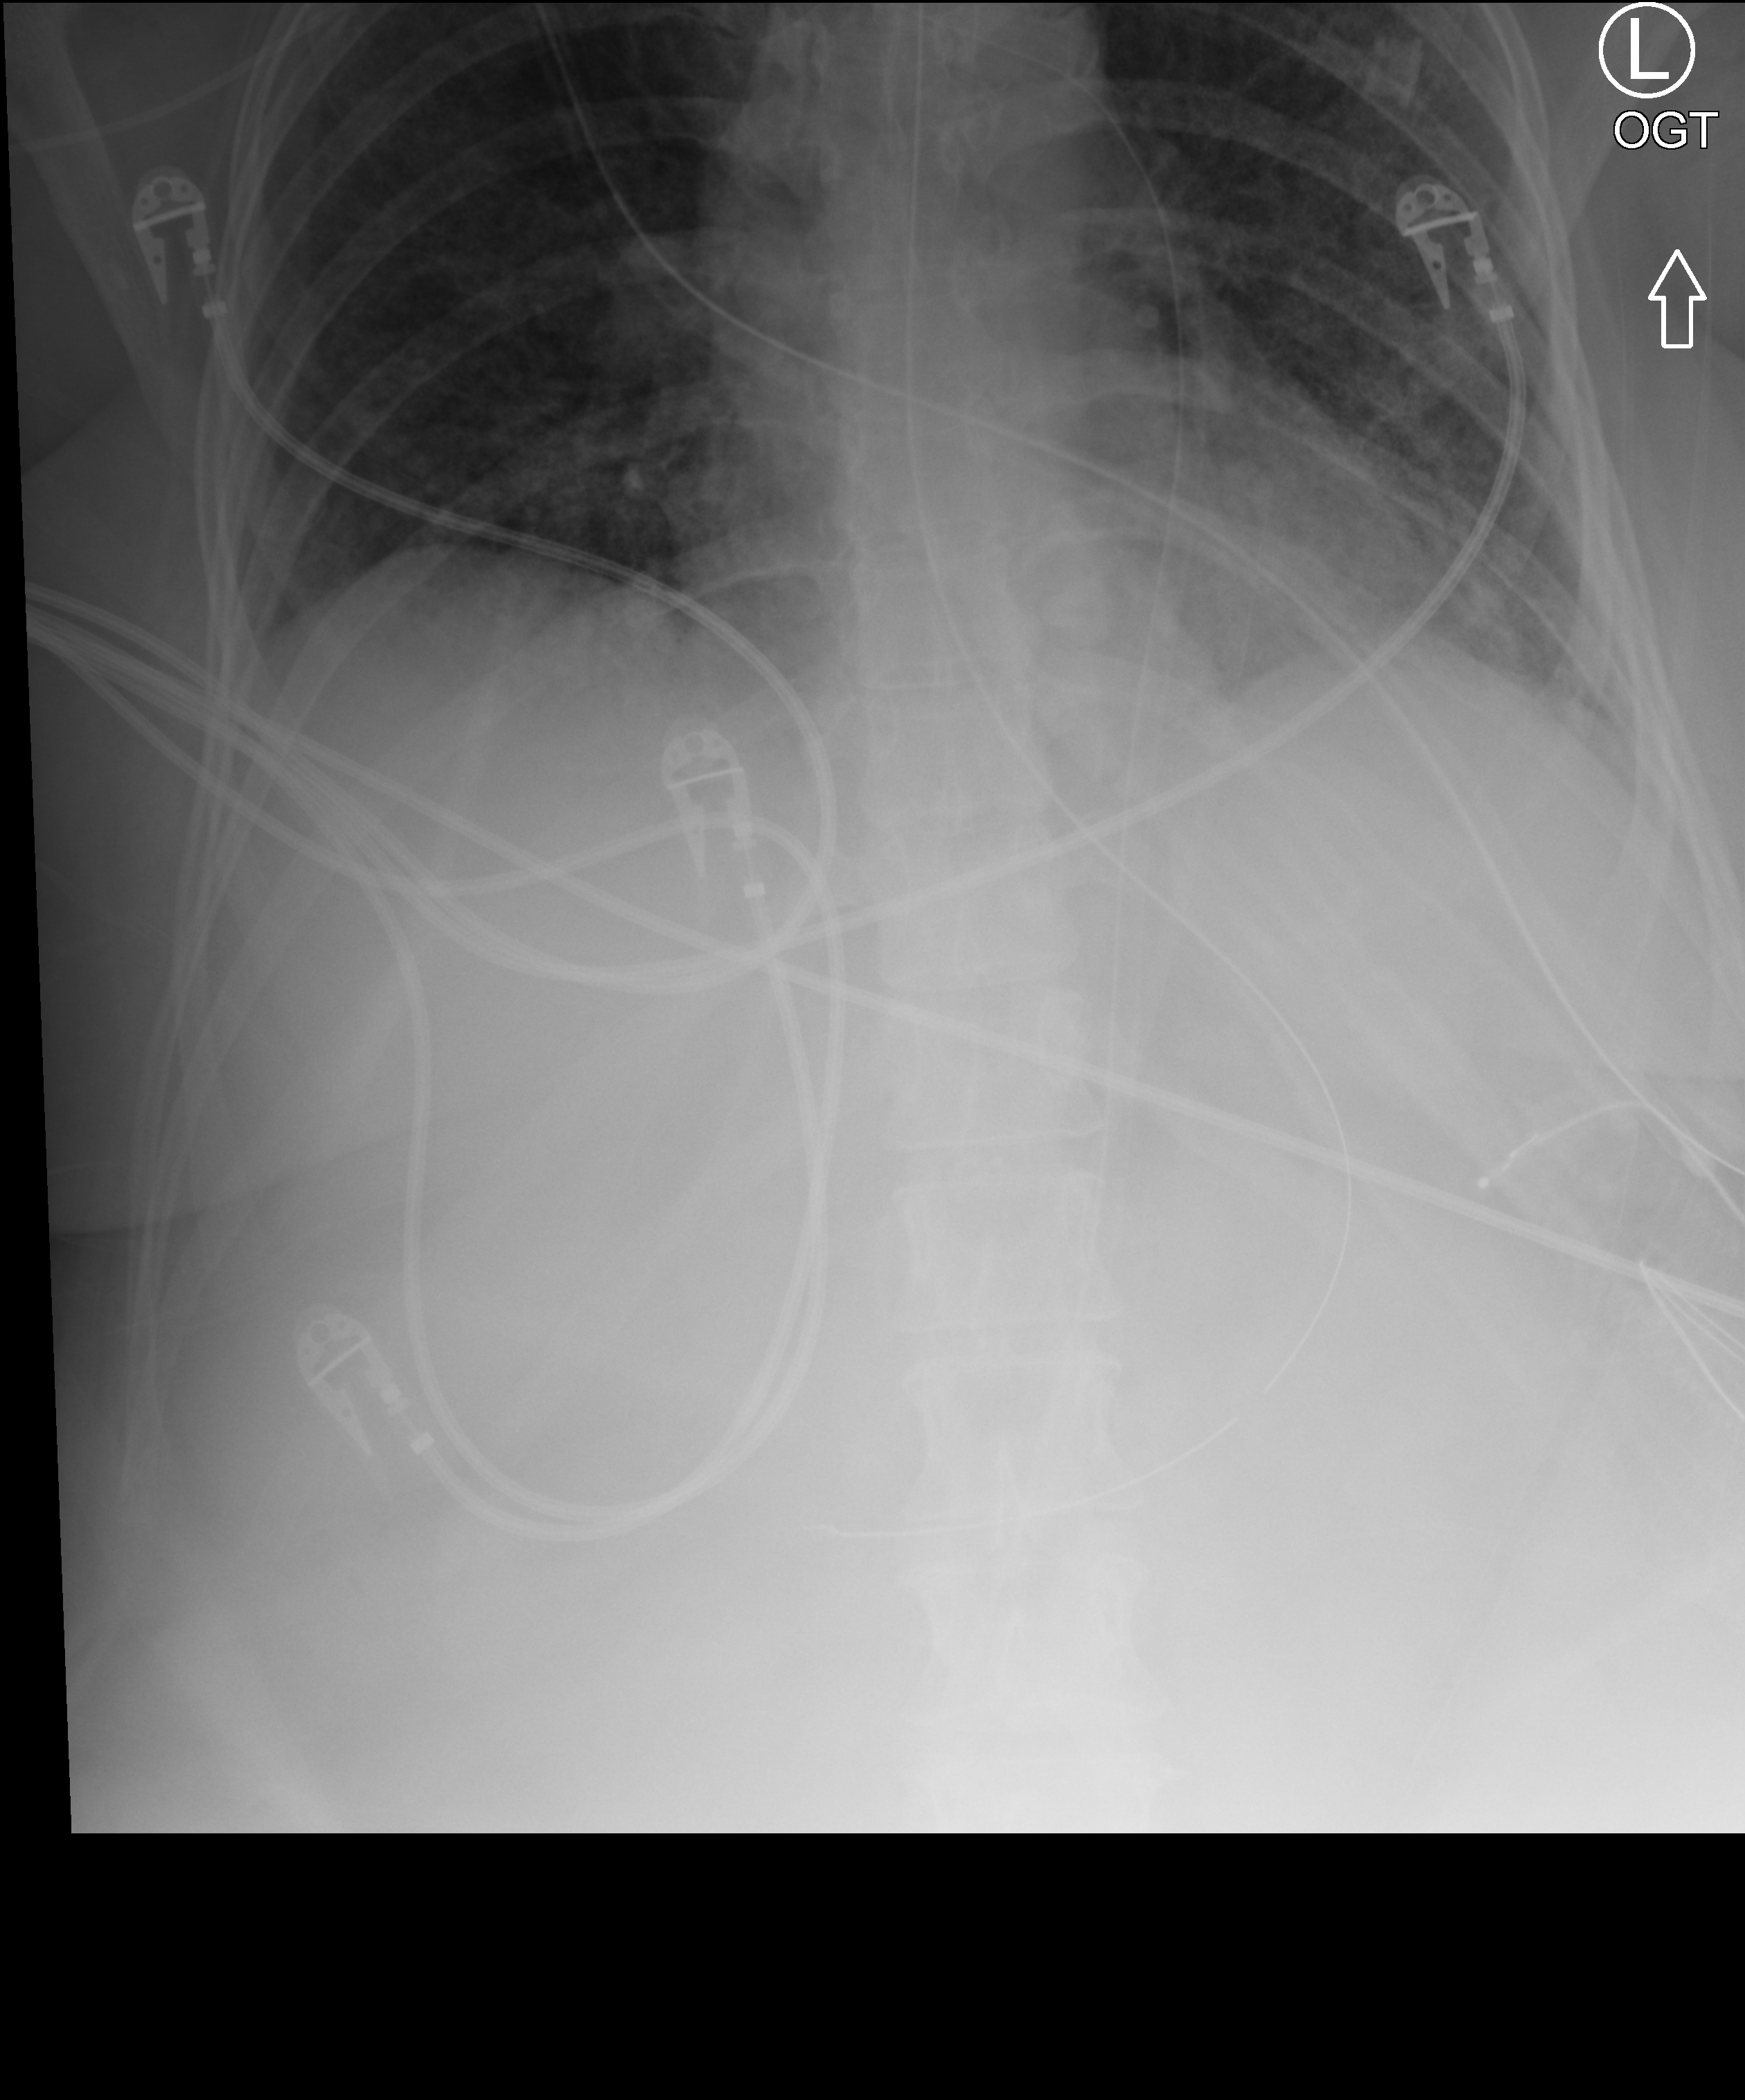
Bedside chest radiograph (computed radiography), anteroposterior (AP) projection. Patient hospitalised with COVID-19; female, aged 18–59 years.
Hospital-stay facts (about this admission, not read from this image; timing relative to this image not recorded): mechanically ventilated during this hospital stay: yes; COPD (admission record): no; length of hospital stay: 73 days.